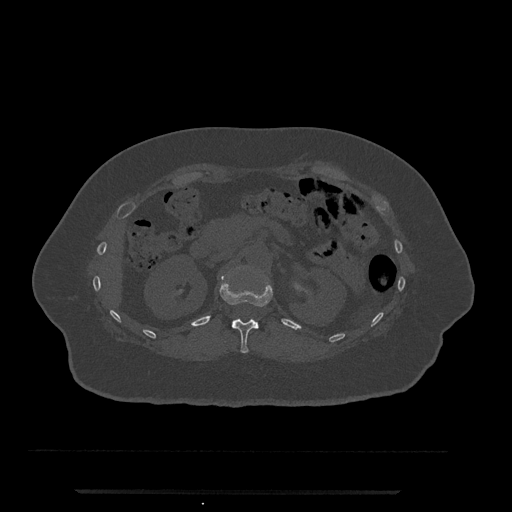
CT including the spine, one axial slice. Slice 152 of 797 in the series (ordered by position). Reconstruction kernel Br40s/3. 120 kVp. Bone window (W 1800 / L 400 HU). 0.5 mm slice thickness. 512 × 512 image matrix, field of view 440 × 440 mm. Female patient, age 51 years. From the clinical record (not read from this slice): primary cancer: neuro; vertebrae with lytic lesions (as recorded): T8.
Structures marked on this image (semi-automatic segmentation, software-assisted and operator-edited):
- T12 vertebra: bounding box <219,276,273,354> (left, top, right, bottom; pixels)